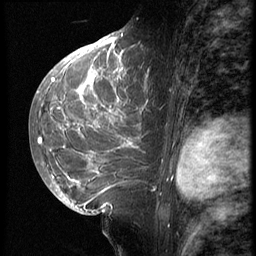
Breast MRI (dynamic contrast-enhanced), one sagittal slice; position 34 of 62 along the scan axis; 3 images stored at this slice position (order not interpretable as contrast timing); 1.5 T; TE 4.2 ms, TR 9 ms; 256 × 256 image matrix, field of view 180 × 180 mm. Female patient, age 28 years. Case-level facts recorded for this patient, not image findings: setting: breast cancer imaged before/during neoadjuvant chemotherapy.
Outlined on this slice (semi-automatically segmented with operator editing):
- analysis volume of interest (the breast-tissue region the enhancement analysis was run in; not a lesion): bounding box (x1, y1, x2, y2) in pixels: (42, 45, 161, 207)
- tumour enhancement mask (voxels above the 140 % enhancement threshold inside the analysis volume of interest): (51, 45, 155, 191)